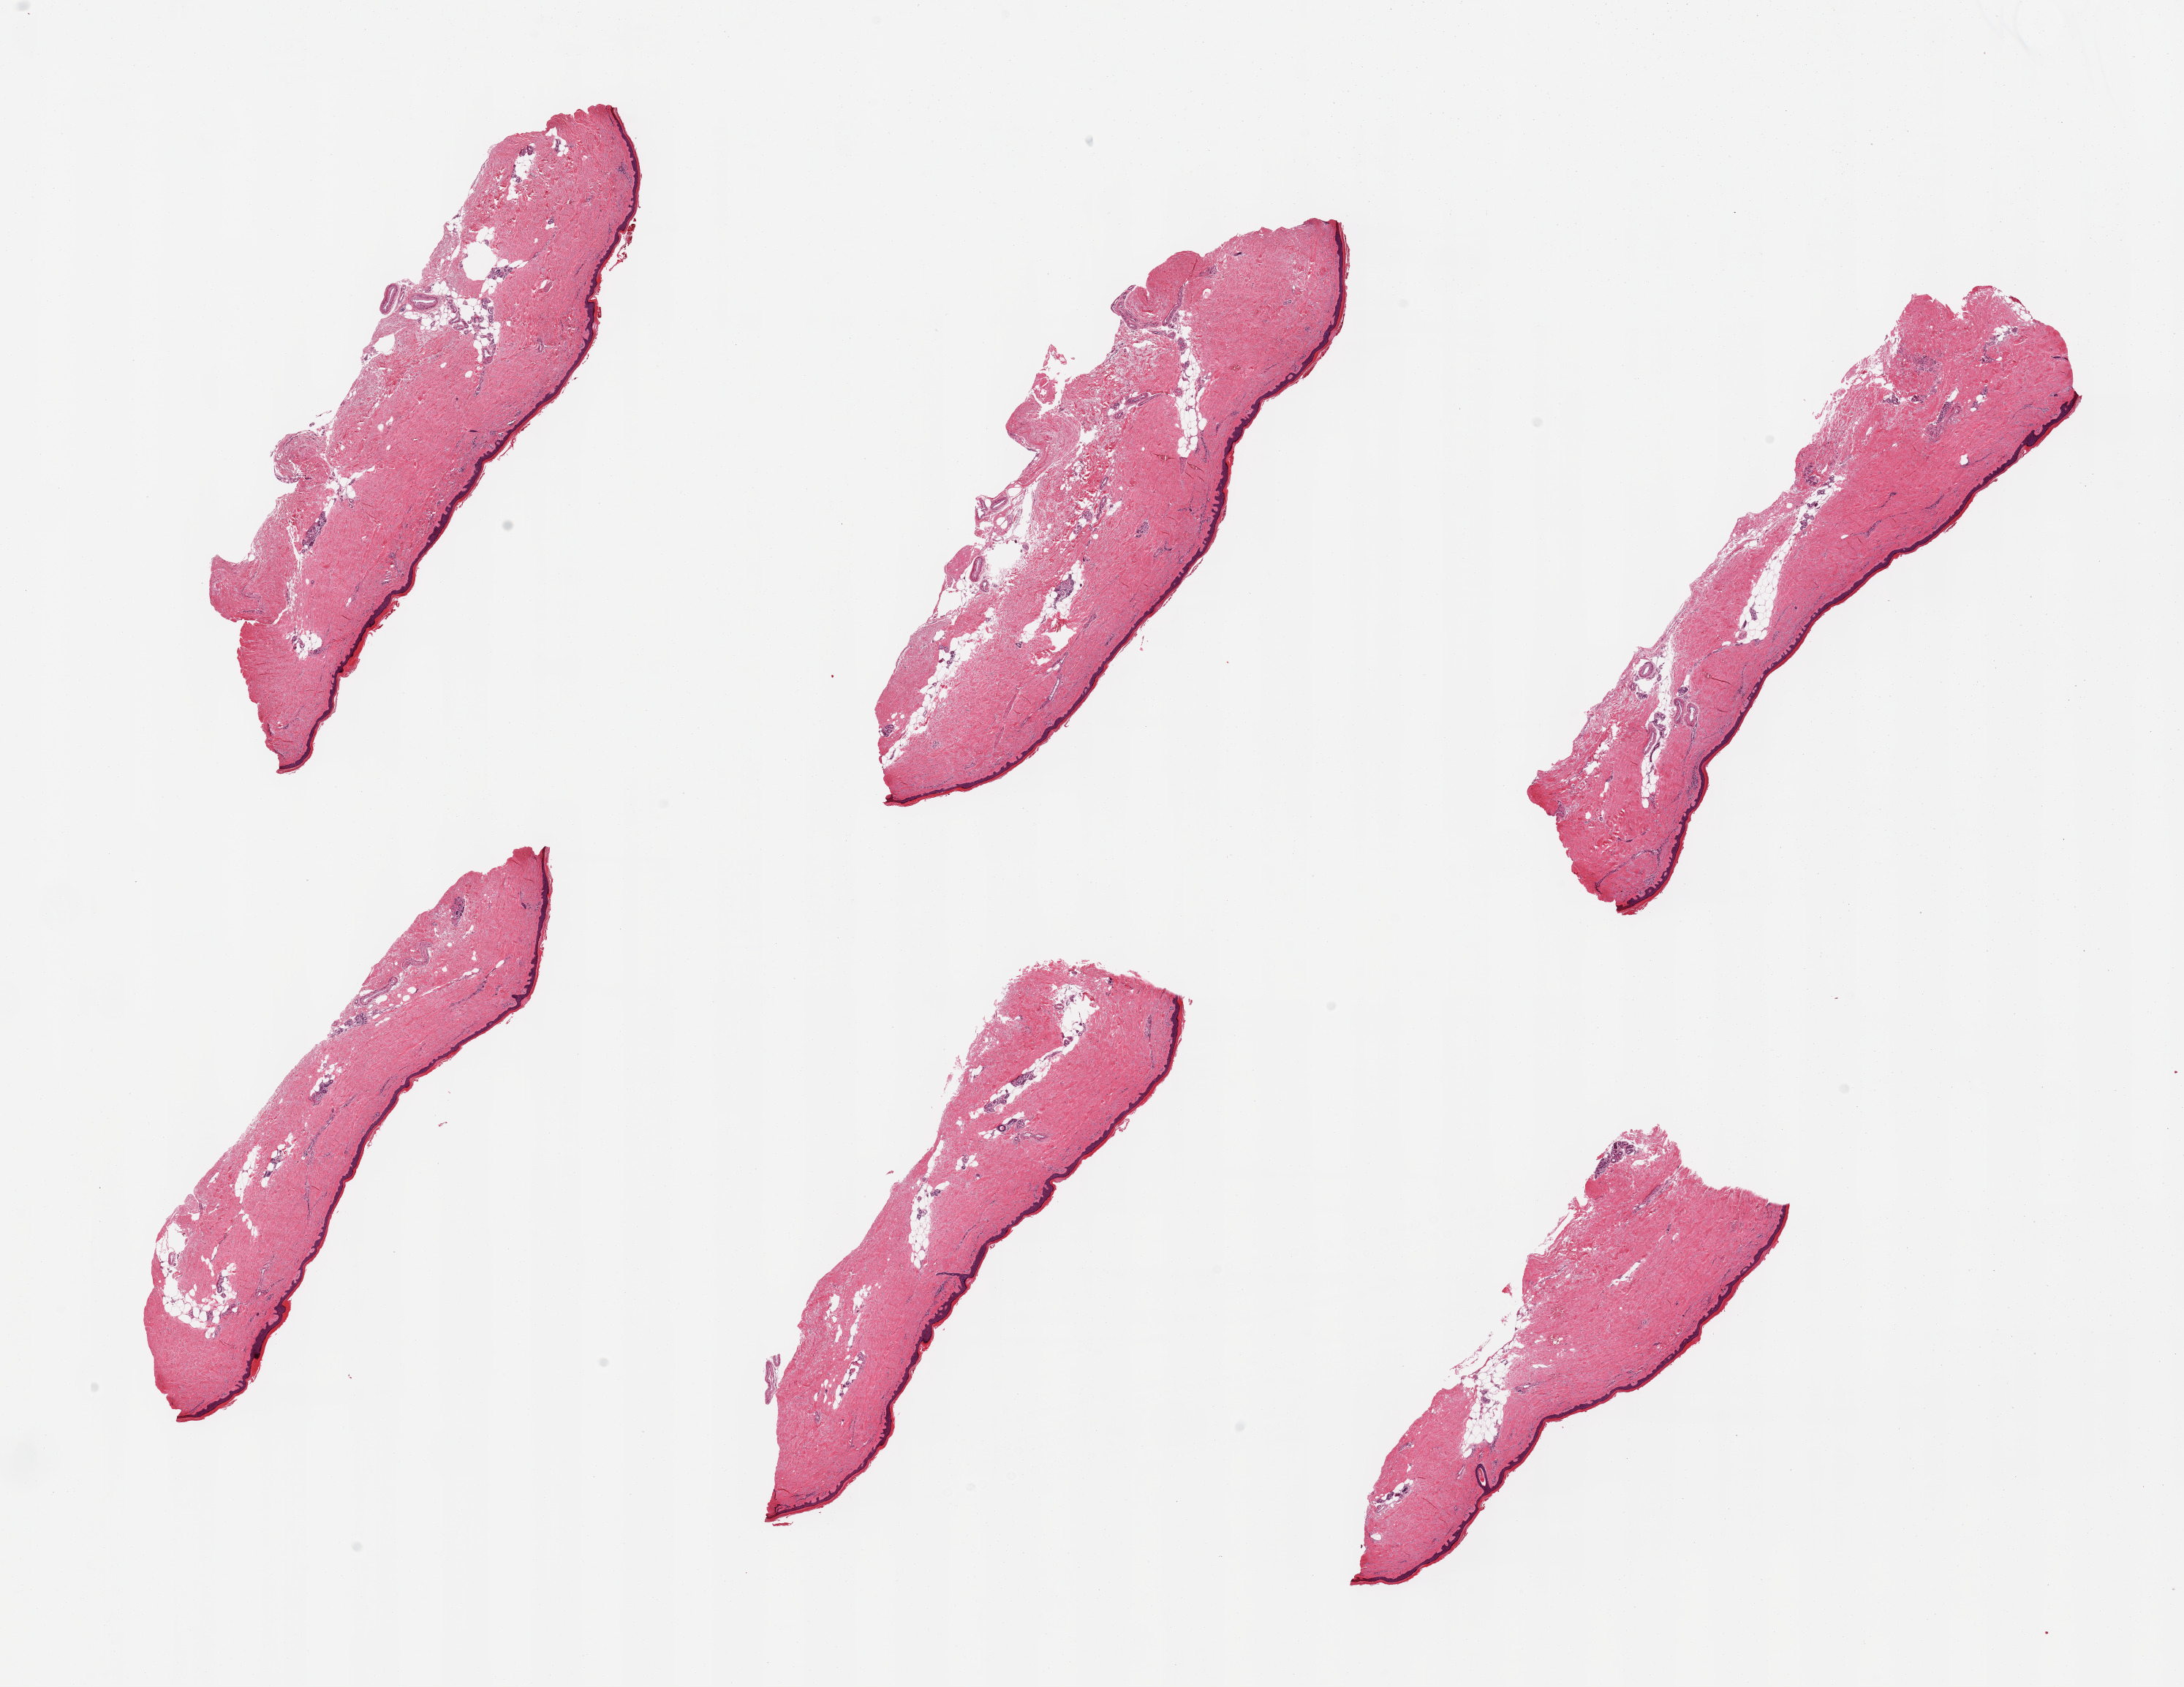
Haematoxylin and eosin whole-slide image — whole scanned area (about 23.6 x 18.2 mm, acquisition: 20x scan) shown as a low-resolution overview. PAXgene-fixed, paraffin-embedded tissue. Sampled site (target tissue): skin of lower leg. Tissue donor sample. Donor: female.
Reviewer comment on this tissue sample: 6 pieces, minimal dermal fat; squamous epithelium is %0-60 microns.